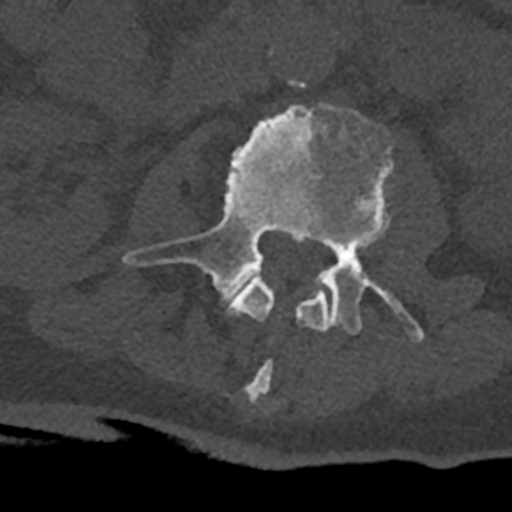
CT including the spine, one axial slice. Reconstruction kernel Br40s/3. Bone window (W 1800 / L 400 HU). 512 × 512 image matrix. Patient: male, 74 years. Case-level facts recorded for this patient, not image findings: primary cancer: renal; vertebrae with lytic lesions (as recorded): T10, L1, L2, L3, L4, L5.
Structures marked on this image (semi-automatically segmented with operator editing):
- L2 vertebra: bounding box [x1, y1, x2, y2] px = [227, 273, 330, 403]
- L3 vertebra: [122, 103, 425, 342]